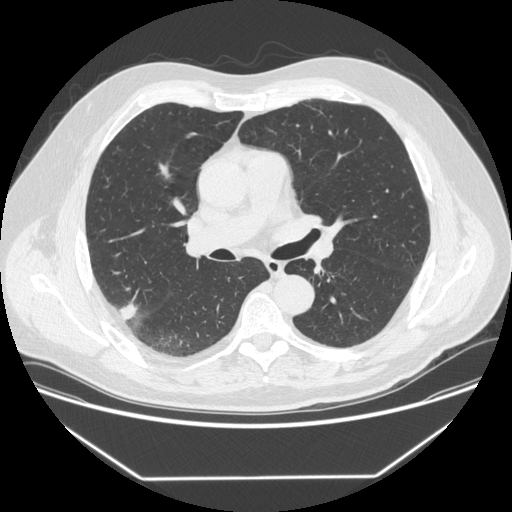
Low-dose screening chest CT, axial slice. Baseline screening round. Lung window (W 1500 / L -600 HU). 1.25 mm slice thickness. Standard (soft-tissue) reconstruction kernel (STANDARD). 512 × 512 image matrix. Male, age 64 years at enrolment.
• Expert-annotated lung lesion, bounding box (x1, y1, x2, y2) in pixels: (101, 298, 142, 330).
• The exam's reader record, not a measurement of the box and not confirmed to be the same lesion: non-calcified nodule or mass ≥4 mm, right upper lobe, 12 × 12 mm, smooth margins, soft tissue attenuation.
• Official screen result: positive, change unspecified: nodule(s) >= 4 mm or enlarging nodule(s), mass(es), or other non-specific abnormalities suspicious for lung cancer.
• Participant outcome: lung cancer diagnosed 92 days after this screen — adenocarcinoma, NOS, right upper lobe, poorly differentiated (G3), stage IIIB (AJCC 6th edition), 15 mm at pathology.